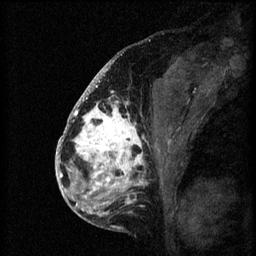
Breast MRI (dynamic contrast-enhanced), one sagittal slice; 3 images stored at this slice position (order not interpretable as contrast timing); 1.5 T; TE 4.2 ms, TR 8.2 ms; 256 × 256 image matrix. Female patient, age 41 years.
Annotated regions visible in this slice (semi-automatic segmentation, software-assisted and operator-edited):
- analysis volume of interest (the breast-tissue region the enhancement analysis was run in; not a lesion): box from (x=72, y=108) to (x=170, y=205) px
- tumour enhancement mask (voxels above the 70 % enhancement threshold inside the analysis volume of interest): (x=72, y=108)–(x=144, y=205)